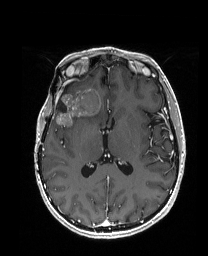
Brain MRI from a brain-tumour surgery series, one axial slice. Position 88 of 192 along the scan axis. T1-weighted post-contrast. 208 × 256 image matrix, field of view 203 × 250 mm. Case-level facts recorded for this patient, not image findings: histopathology: Metastatic Carcinoma from Breast primary.
Structures marked on this image (outlined manually by an expert reader):
- previous resection cavity: box from (x=57, y=85) to (x=68, y=112) px
- tumour: (x=55, y=87)–(x=104, y=127)